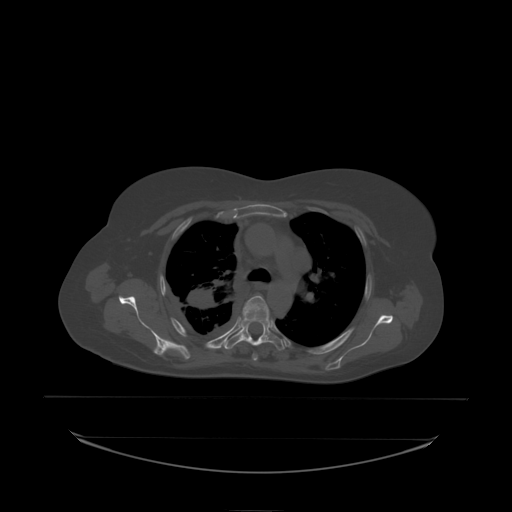
CT including the spine, one axial slice. Slice 161 of 242 in the series (ordered by position). Bone window (W 1800 / L 400 HU). 2.5 mm slice thickness. 512 × 512 image matrix, field of view 500 × 500 mm. Female patient, age 53 years. Case-level facts recorded for this patient, not image findings: primary cancer: lung.
Structures marked on this image (semi-automatically segmented with operator editing):
- T4 vertebra: box from (x=243, y=296) to (x=270, y=317) px
- T5 vertebra: (x=236, y=313)–(x=272, y=338)